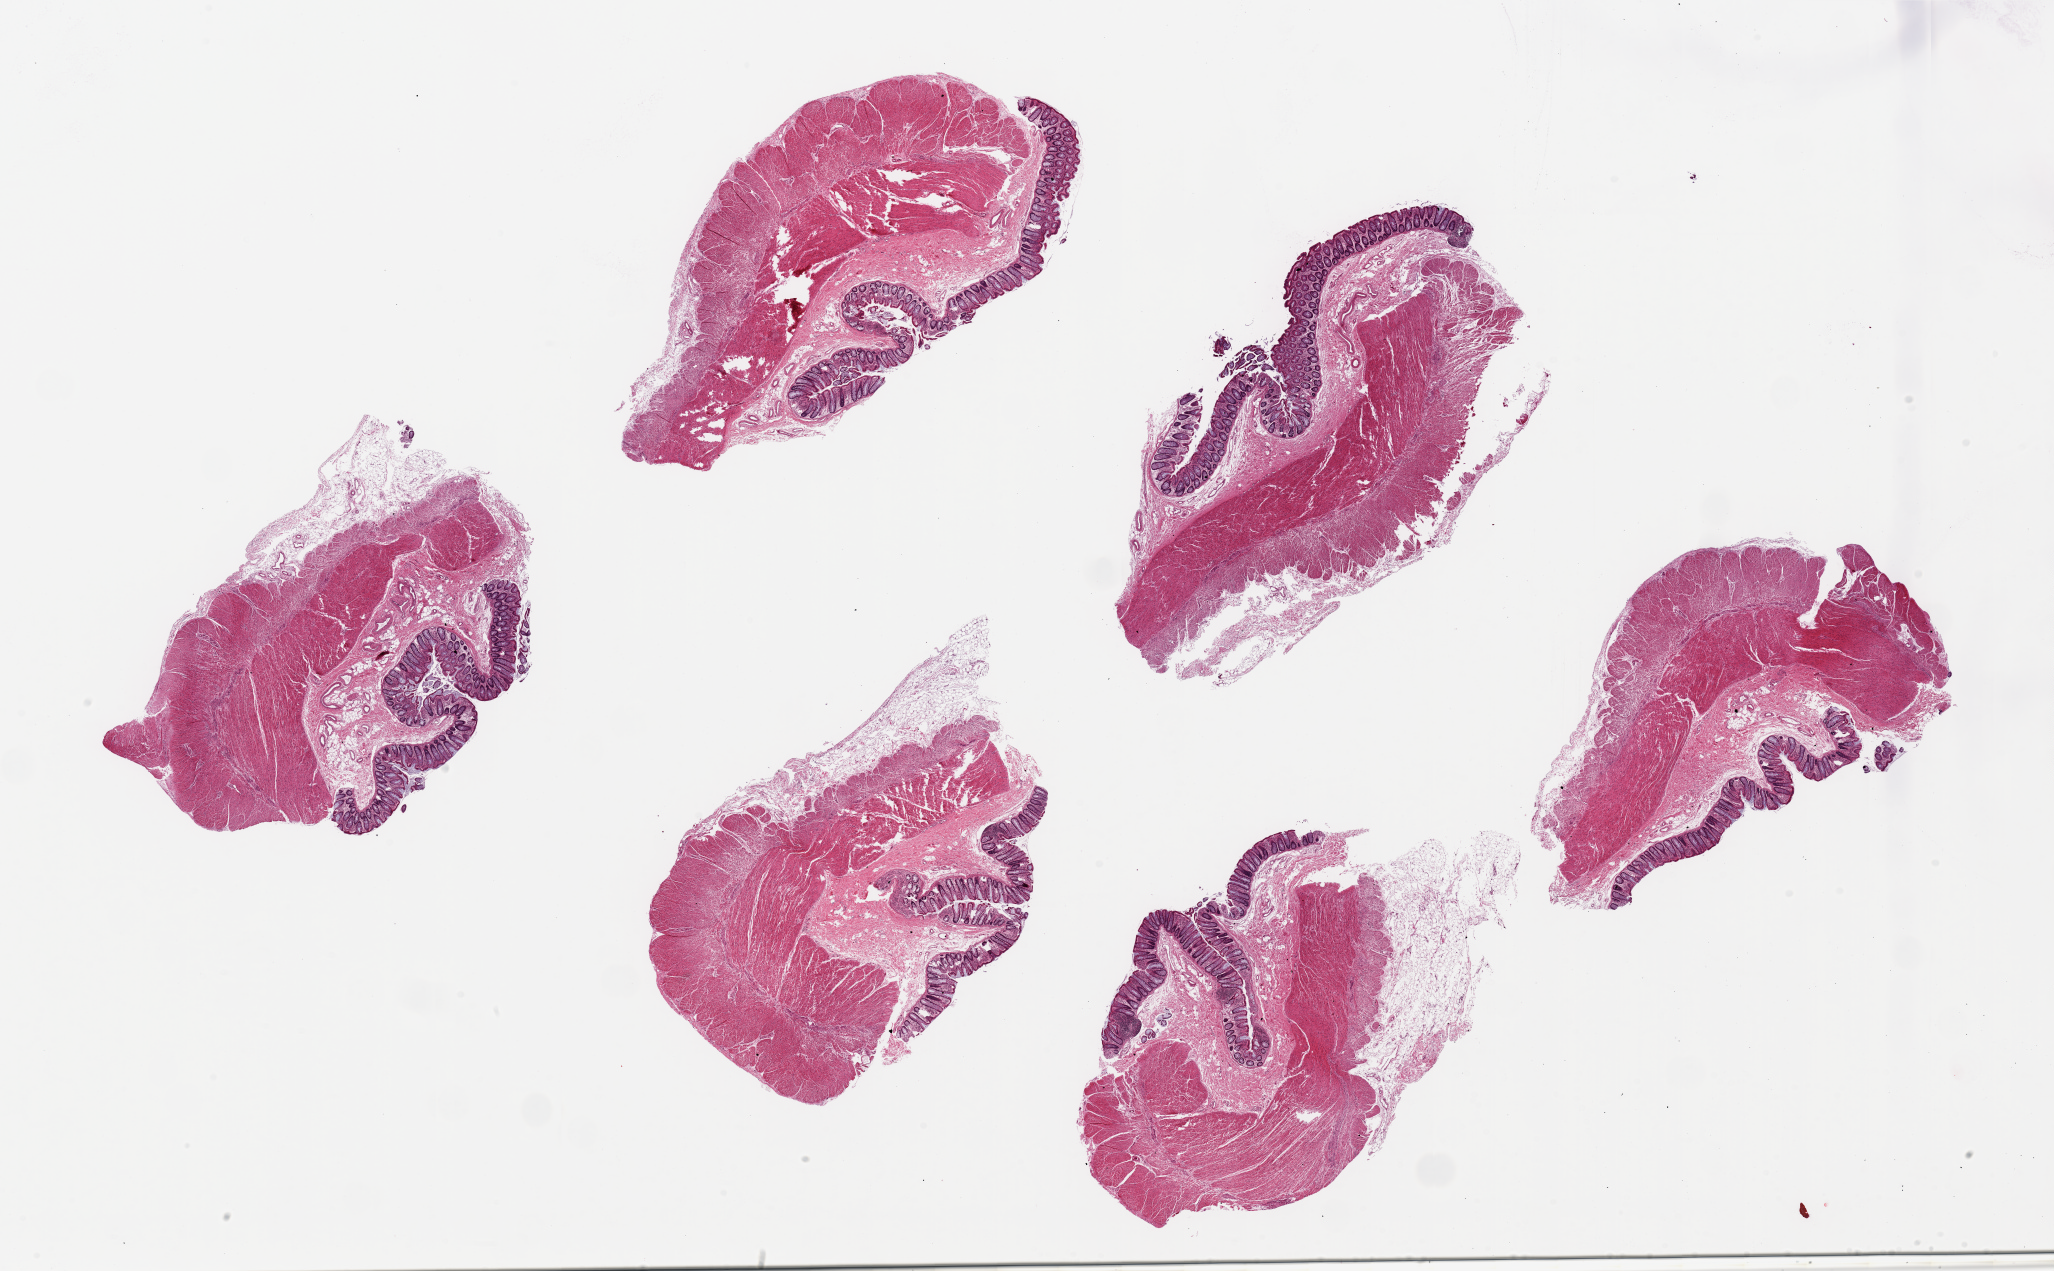
Whole-slide image, hematoxylin and eosin (H&E) stain — shown as a low-resolution overview of the whole scanned area (about 32.5 x 20.1 mm, from a 20x scan), PAXgene-fixed paraffin-embedded (PFPE) section, sampled site (target tissue): sigmoid colon, tissue donor sample. Donor sex: male.
Pathologist's review note for this sample: 6 pieces ~7x5mm, 60-70% muscularis, rest is fat/mucosa.